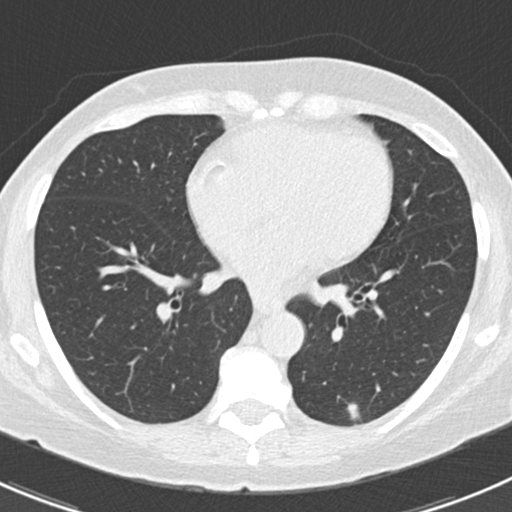
Low-dose screening chest CT, one axial slice. Slice 80 of 166 in the series (ordered by position). Reconstruction kernel B30f. Lung window (W 1500 / L -600 HU). 2 mm slice thickness. 512 × 512 image matrix, field of view 307 × 307 mm.
Outlined on this slice (manually delineated by an expert):
- lesion 1 (tumor, lower lobe of left lung): bounding box (x1, y1, x2, y2) in pixels: (347, 403, 360, 420)